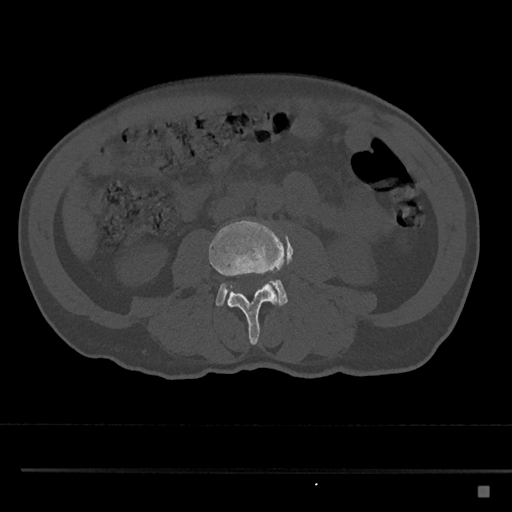
CT including the spine, one axial slice; slice 677 of 797 in the series (ordered by position); reconstruction kernel Br40s/3; bone window (W 1800 / L 400 HU); 512 × 512 image matrix, field of view 391 × 391 mm. Male patient, age 59 years. Case-level facts recorded for this patient, not image findings: primary cancer: prostate.
Annotated regions visible in this slice (semi-automatic segmentation, software-assisted and operator-edited):
- L3 vertebra: bounding box (x1, y1, x2, y2) in pixels: (208, 219, 285, 345)
- L4 vertebra: (215, 279, 288, 307)